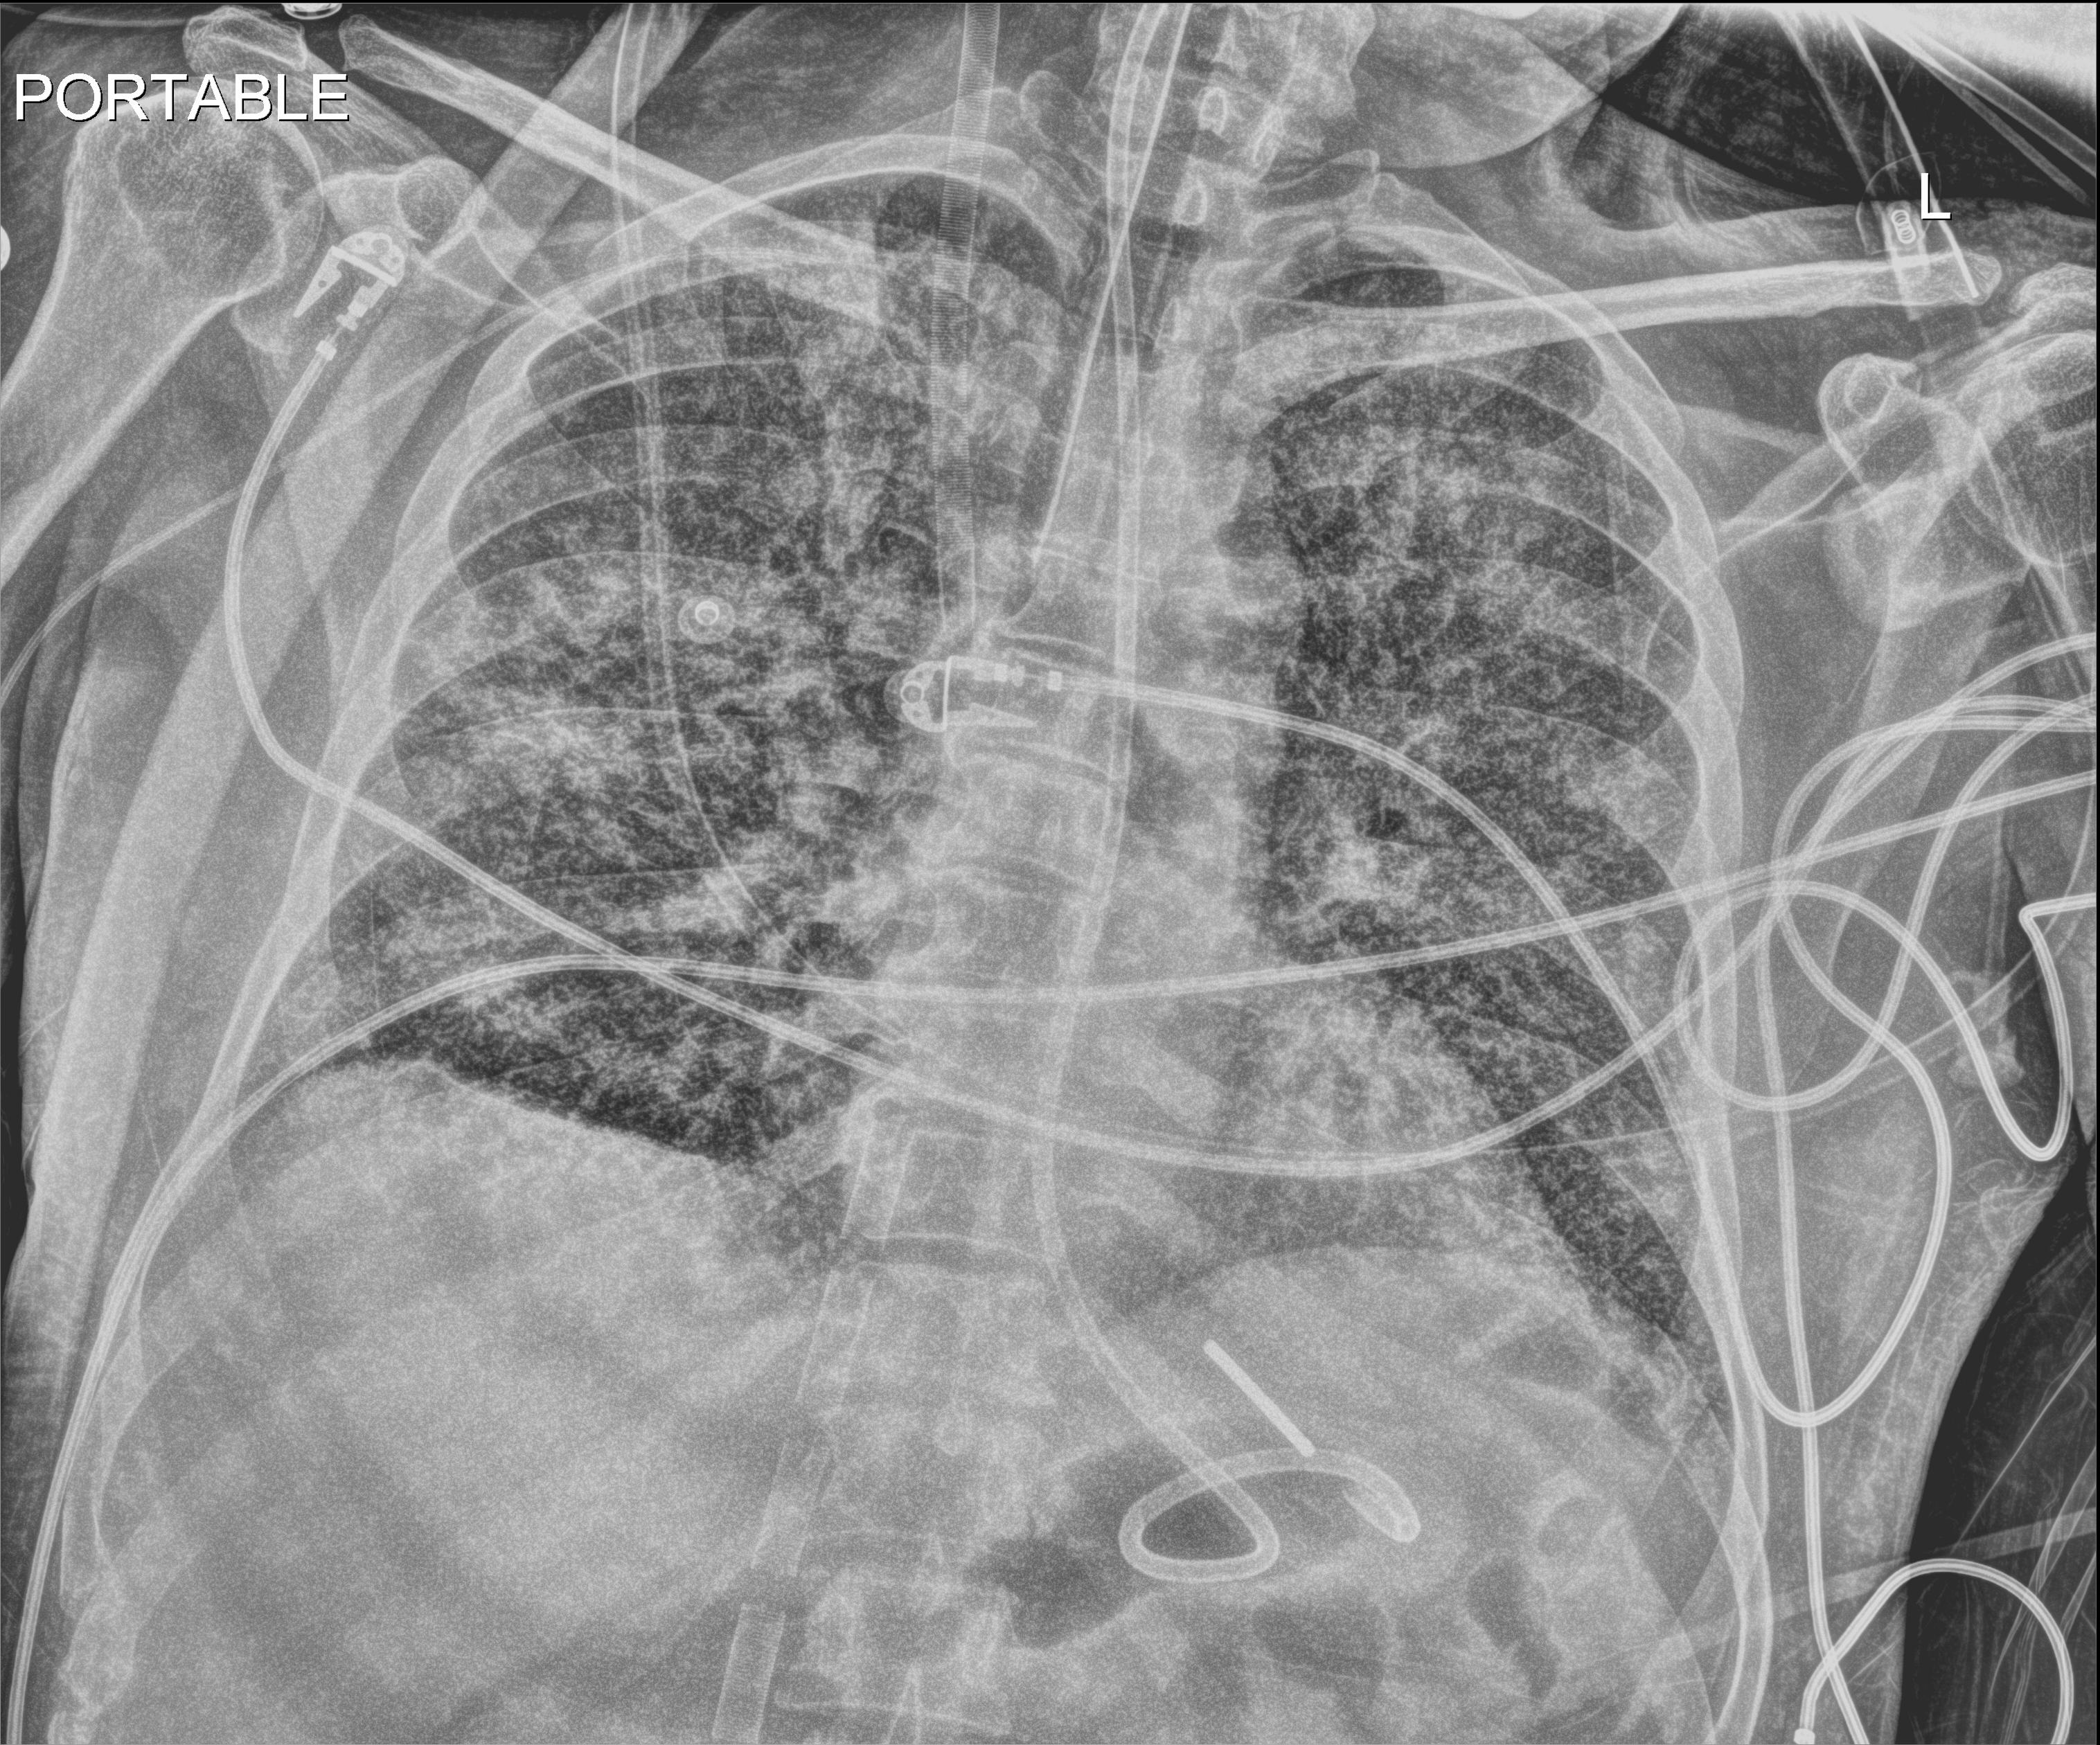
Portable chest radiograph; anteroposterior (AP) projection. Male patient hospitalised with COVID-19, age 18–59 years.
From the hospital-stay record, not from the radiograph (when in the stay this image was taken is not recorded):
- admitted to intensive care during this hospital stay: yes
- hypertension (admission record): no